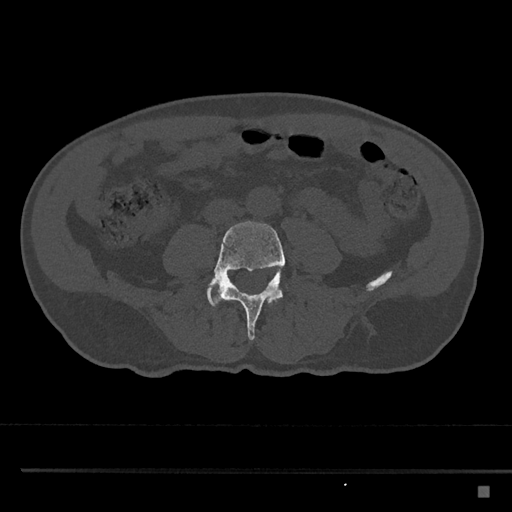
CT including the spine, one axial slice. Position 633 of 797 along the scan axis. Reconstruction kernel Br40s/3. Bone window (W 1800 / L 400 HU). 0.5 mm slice thickness. 512 × 512 image matrix, field of view 391 × 391 mm. Patient: male, 59 years. From the clinical record (not read from this slice): primary cancer: prostate.
Structures marked on this image (semi-automatically segmented with operator editing):
- L4 vertebra: box from (x=212, y=221) to (x=285, y=341) px
- L5 vertebra: (x=207, y=274)–(x=219, y=307)